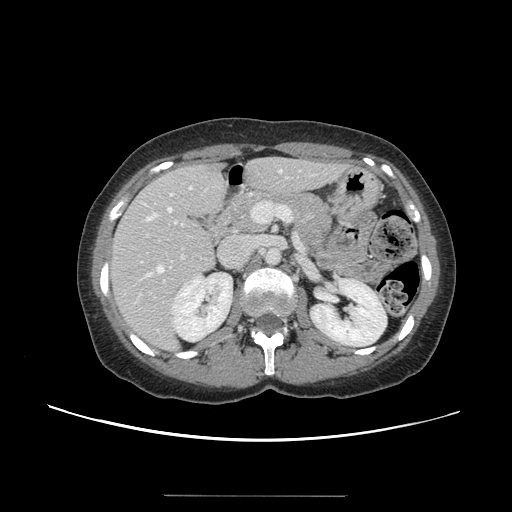
Contrast-enhanced abdominal CT, one axial slice. Slice 73 of 144 in the series (ordered by position). 120 kVp. Intravenous contrast given. Soft-tissue window (W 400 / L 40 HU). 2.5 mm slice thickness. 512 × 512 image matrix, field of view 380 × 380 mm. Female patient, age 53 years. Case-level facts recorded for this patient, not image findings: diagnosis: colorectal cancer liver metastases, imaged before liver resection; multiple liver metastases: yes; largest metastasis: 1.1 cm.
Structures marked on this image (manually delineated by an expert):
- hepatic veins: box from (x=147, y=169) to (x=282, y=276) px
- liver: (x=110, y=159)–(x=341, y=349)
- planned liver remnant (the part of the liver to remain after resection): (x=110, y=158)–(x=321, y=301)
- portal vein (with intrahepatic branches): (x=140, y=201)–(x=292, y=294)